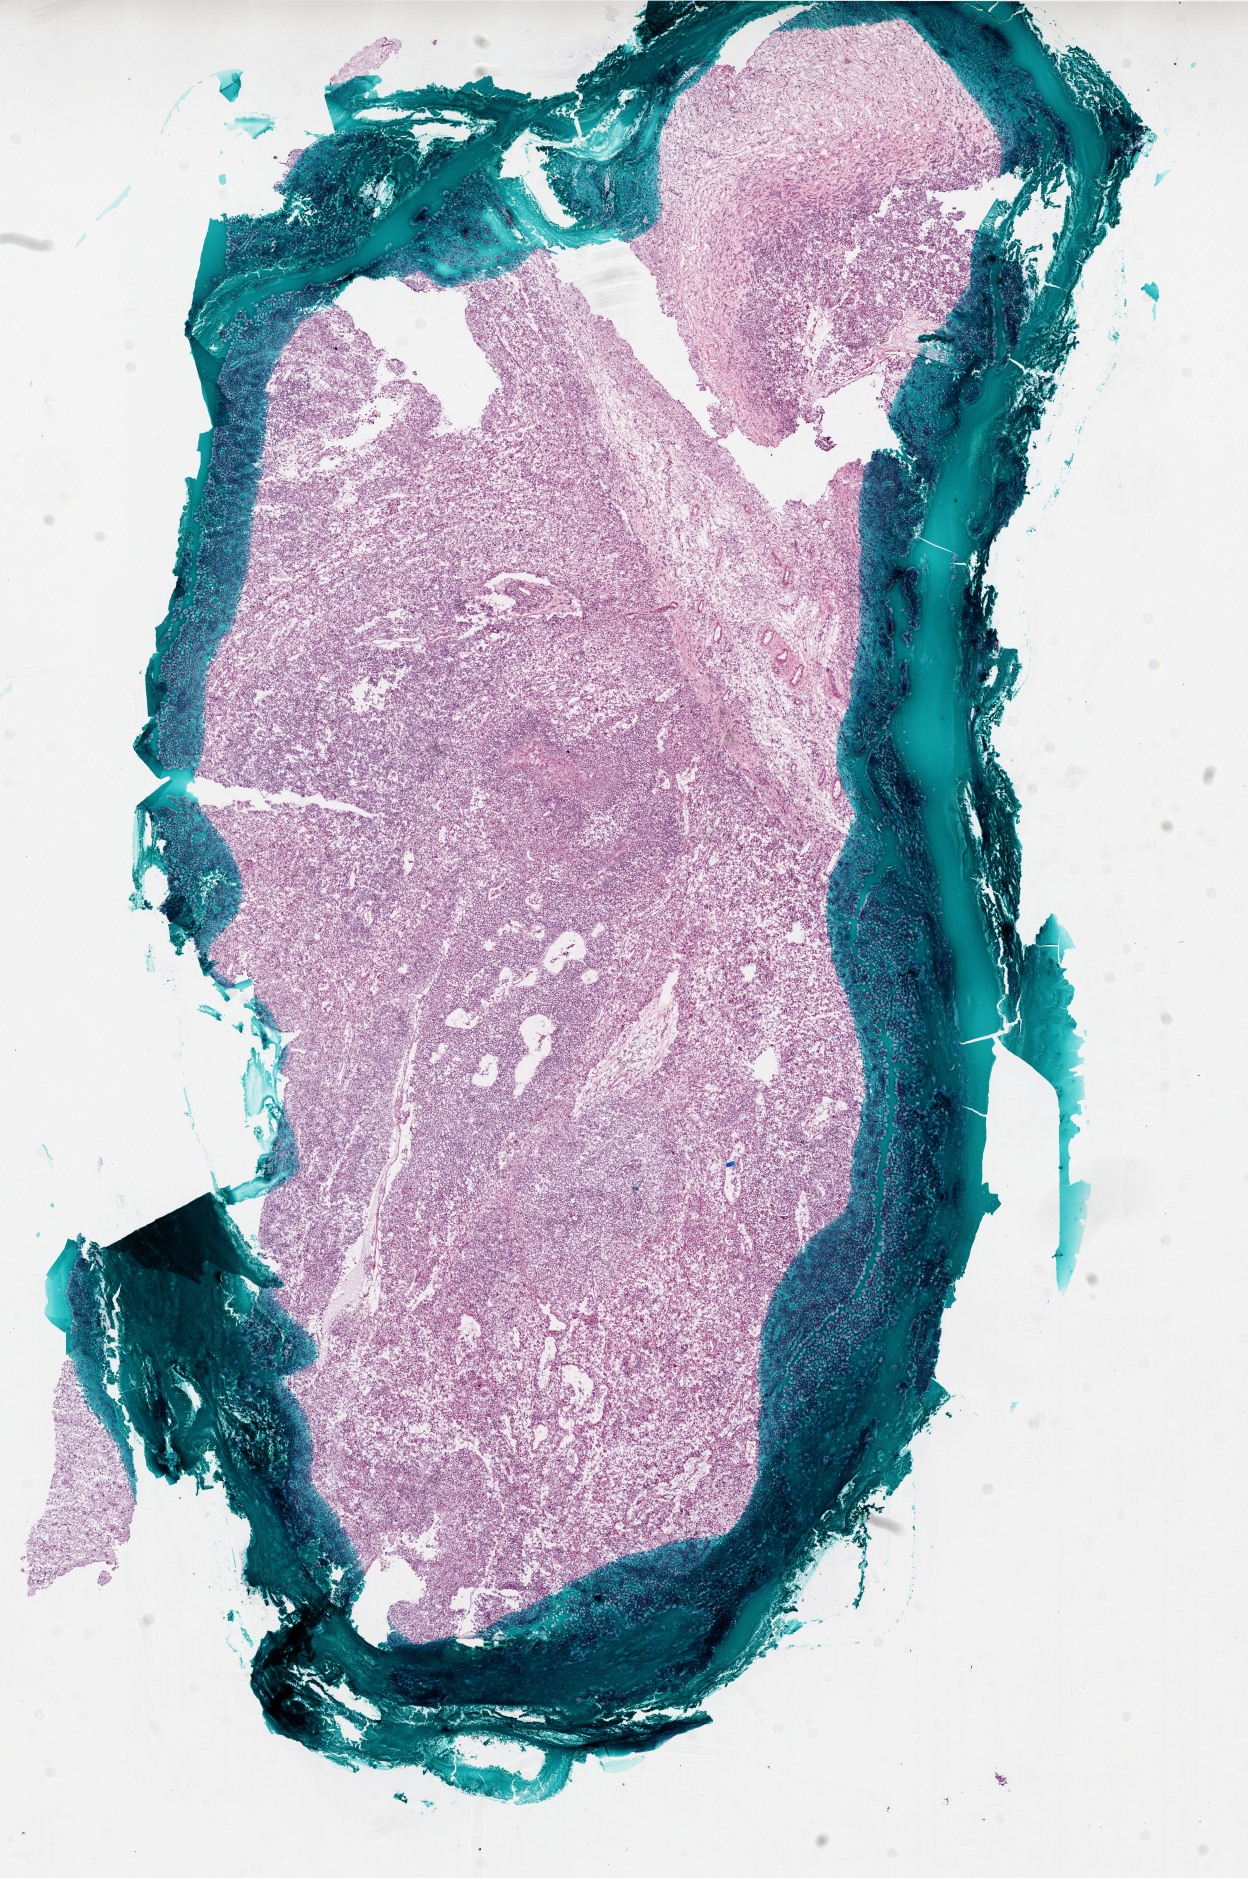
H&E whole-slide image — low-resolution overview of the scanned area, about 10.0 x 15.0 mm (slide scanned at 20x), frozen section from the bottom of the tissue portion, sample: primary tumour, brain. Male, age 46 years at initial diagnosis. Pathologist review of this section (percent, as recorded): tumour cells 80%, tumour nuclei 95%, normal cells 0%, stromal cells 15%, necrosis 5%.
Histologic diagnosis: Glioblastoma.